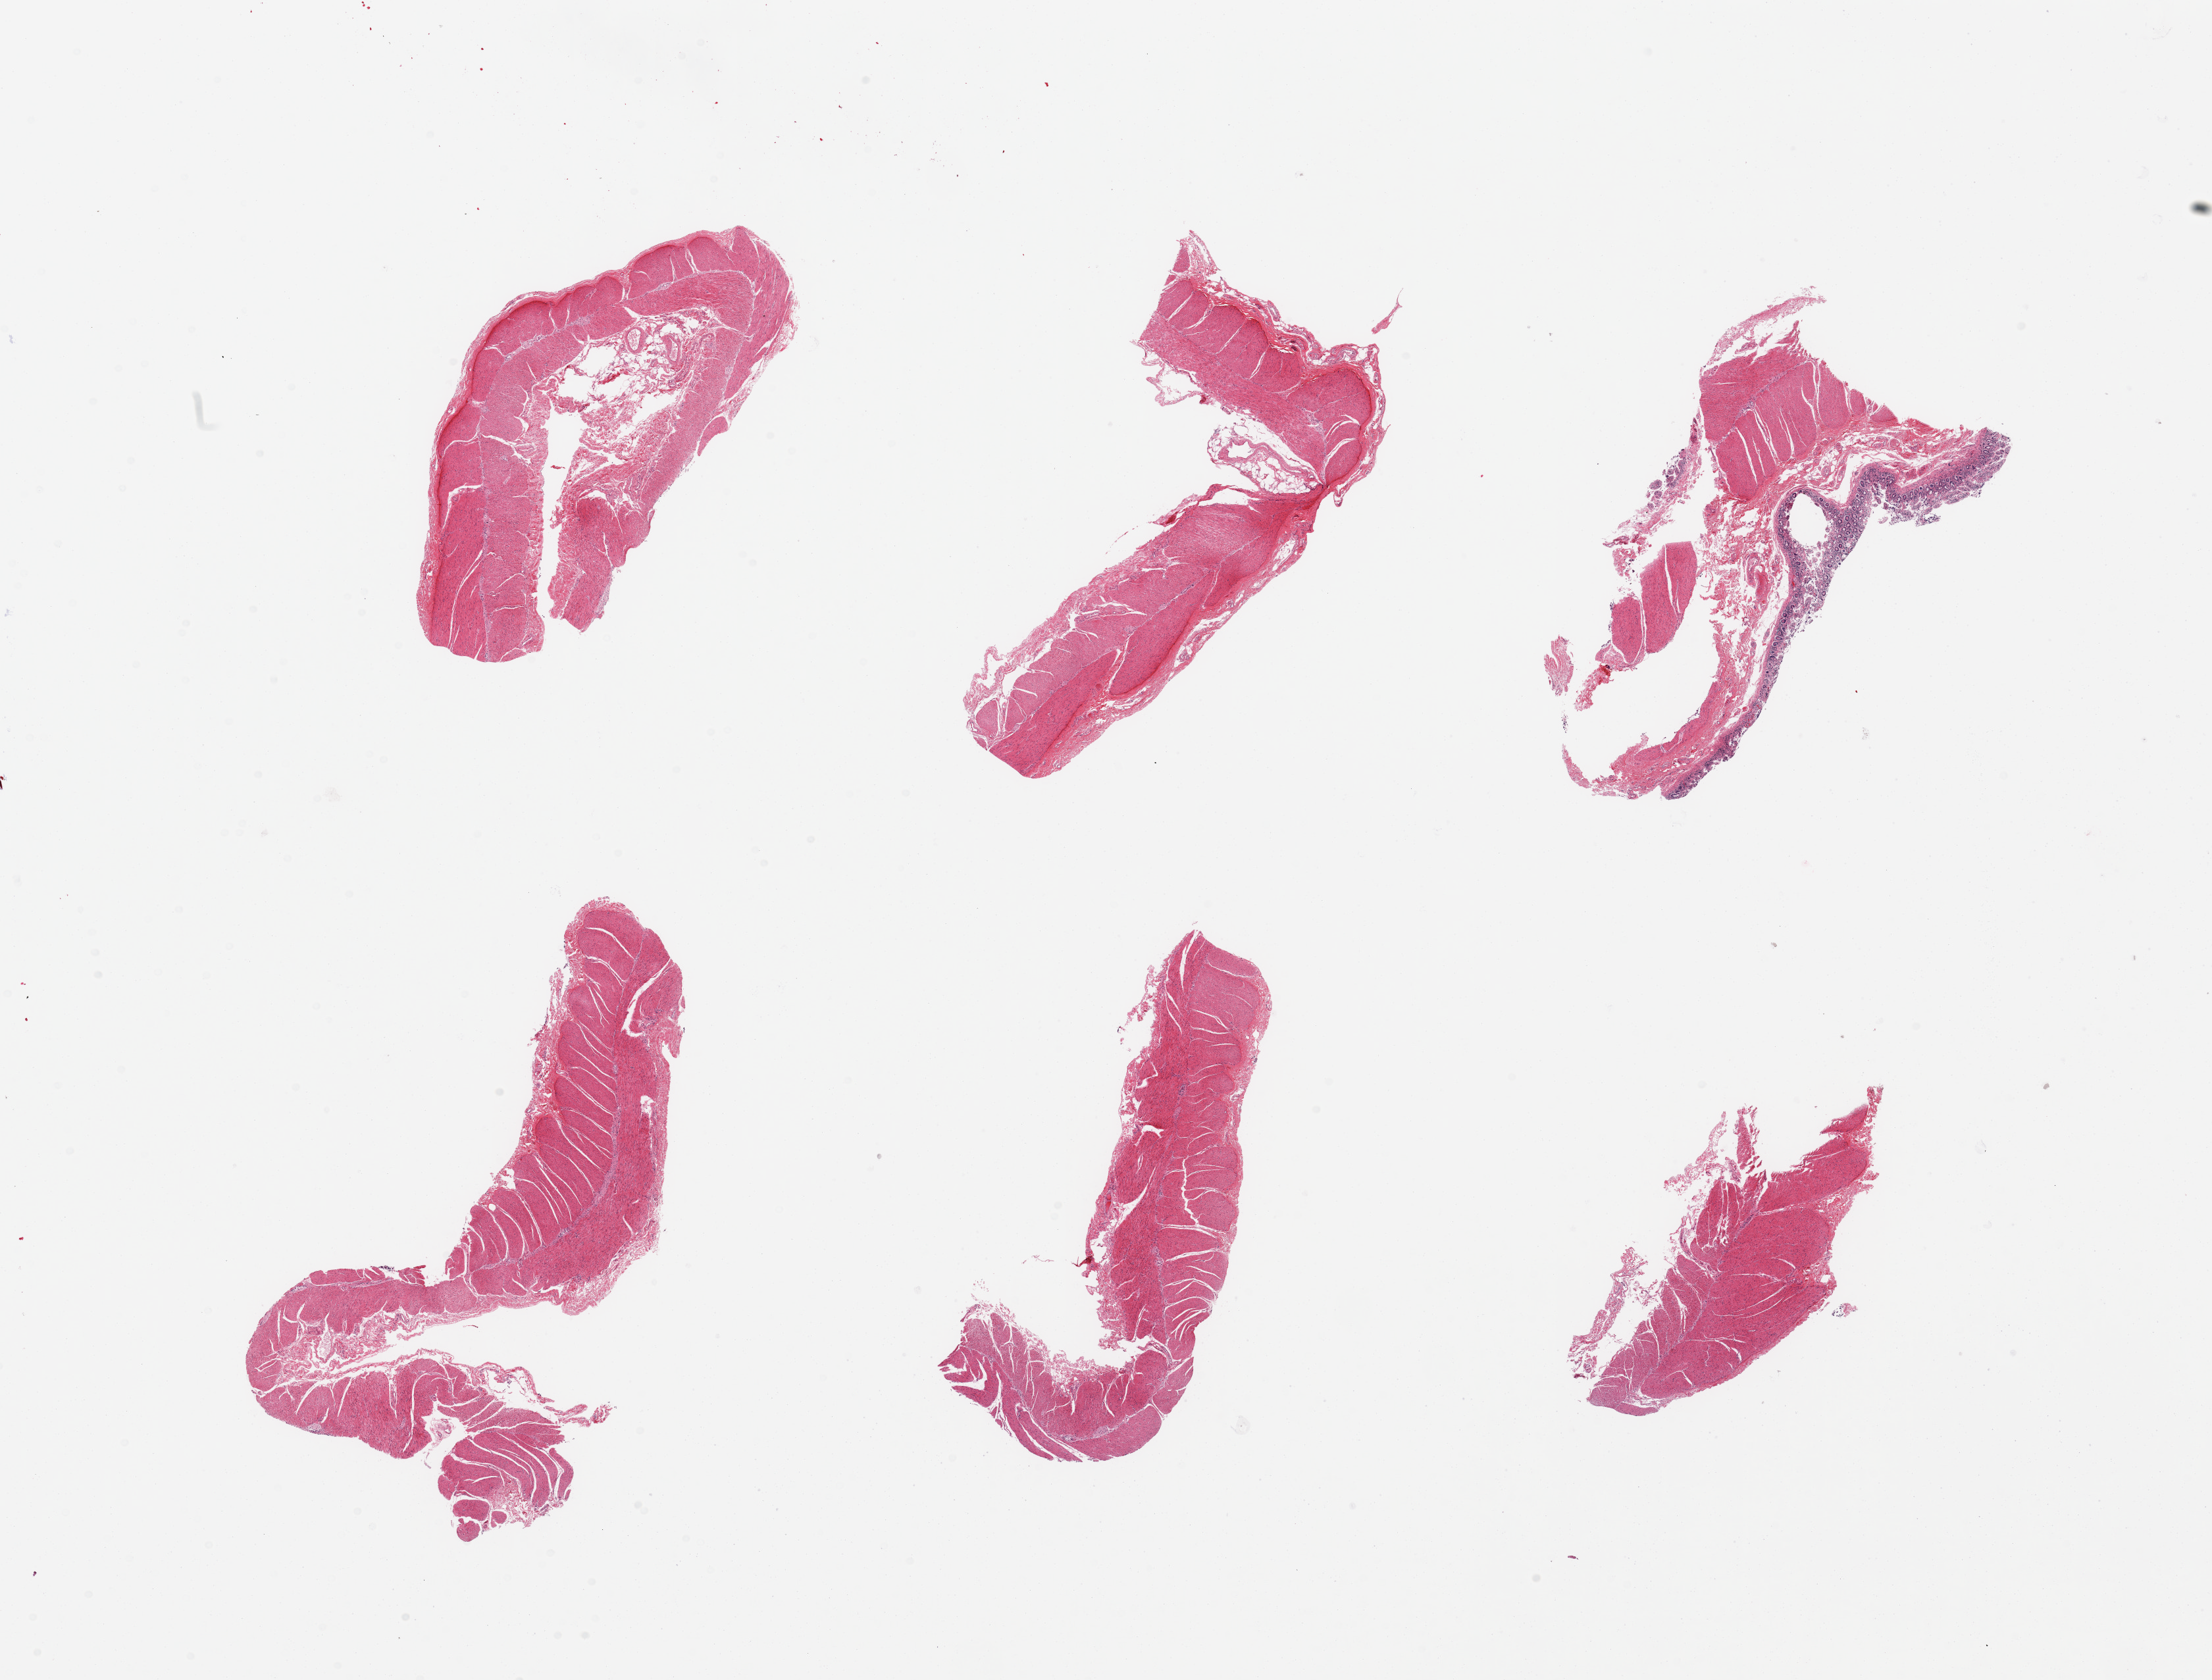
Whole-slide image, H&E stain, brightfield, whole scanned area (about 26.6 x 20.2 mm, acquisition: 20x scan) shown as a low-resolution overview; PAXgene-fixed, paraffin-embedded tissue; target tissue: ileum; tissue donor sample. Male donor.
Review note (as recorded): 6 pieces, trace mucosa, no target lymphoid aggregates.